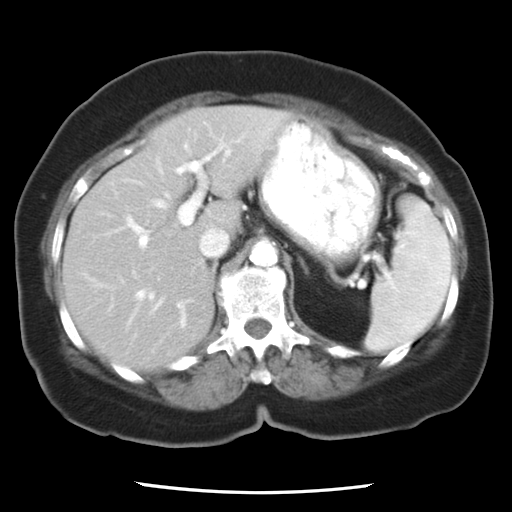
Contrast-enhanced abdominal CT, one axial slice. Slice 15 of 24 in the series (ordered by position). 120 kVp. Soft-tissue window (W 400 / L 40 HU). 7.5 mm slice thickness. 512 × 512 image matrix, field of view 312 × 312 mm. Female patient, age 71 years. From the clinical record (not read from this slice): diagnosis: colorectal cancer liver metastases, imaged before liver resection; multiple liver metastases: no; largest metastasis: 4.3 cm; chemotherapy before resection: no.
Structures marked on this image (expert manual segmentation):
- hepatic veins: bounding box <123,178,185,361> (left, top, right, bottom; pixels)
- liver: <64,107,293,370>
- planned liver remnant (the part of the liver to remain after resection): <64,119,242,370>
- portal vein (with intrahepatic branches): <86,143,225,327>